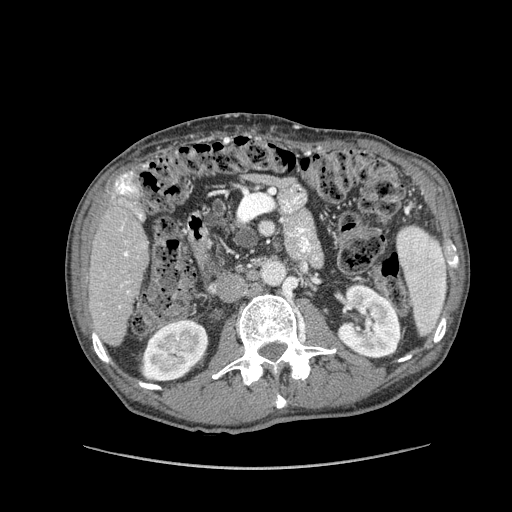
Contrast-enhanced abdominal CT (liver protocol), one axial slice. Position 33 of 162 along the scan axis. Reconstruction kernel STANDARD. 100 kVp. Soft-tissue window (W 400 / L 40 HU). 2.5 mm slice thickness. 512 × 512 image matrix, field of view 400 × 400 mm. From the clinical record (not read from this slice): diagnosis: hepatocellular carcinoma (patient treated with transarterial chemoembolisation; whether this scan precedes or follows treatment is not stated here); TNM stage (as recorded): Stage-IIIA; Child-Pugh class: A.
Annotated regions visible in this slice (semi-automatic segmentation, software-assisted and operator-edited):
- liver parenchyma outside the tumour (the mass and vessels are separate outlines, so this box may not span the whole liver): bounding box (x1, y1, x2, y2) in pixels: (88, 170, 148, 344)
- liver vessels: (115, 172, 142, 308)